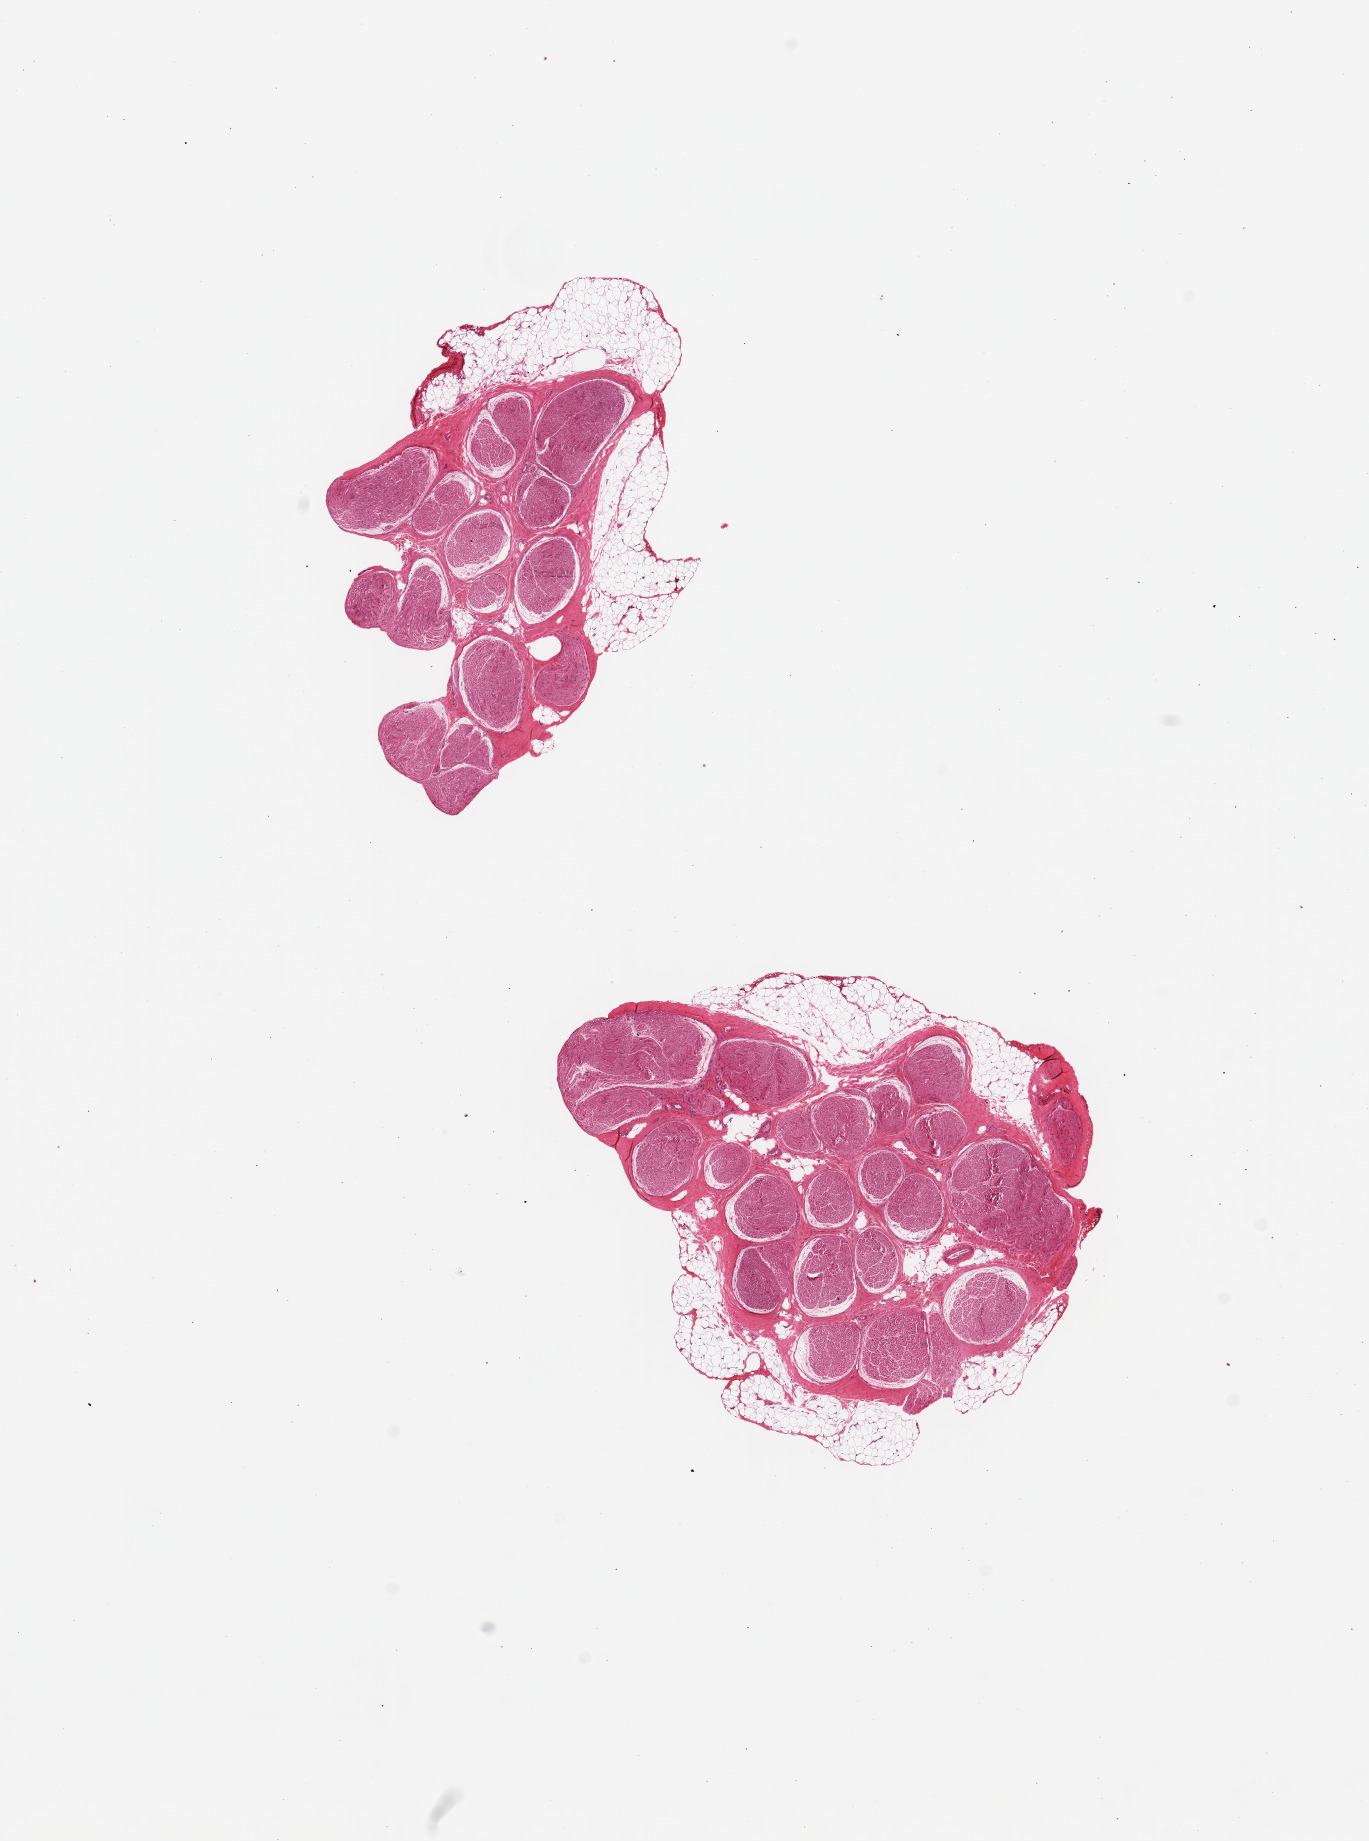
Whole-slide image, haematoxylin and eosin stain, brightfield — a low-resolution overview of the entire scanned area, about 10.8 x 14.6 mm (acquisition: 20x scan). PAXgene-fixed, paraffin-embedded tissue. Target tissue: tibial nerve. Donor tissue sample. Donor: female.
Pathologist's review note for this sample: 2 pieces, discontinuous rims of adherent fat up to ~0.7mm.